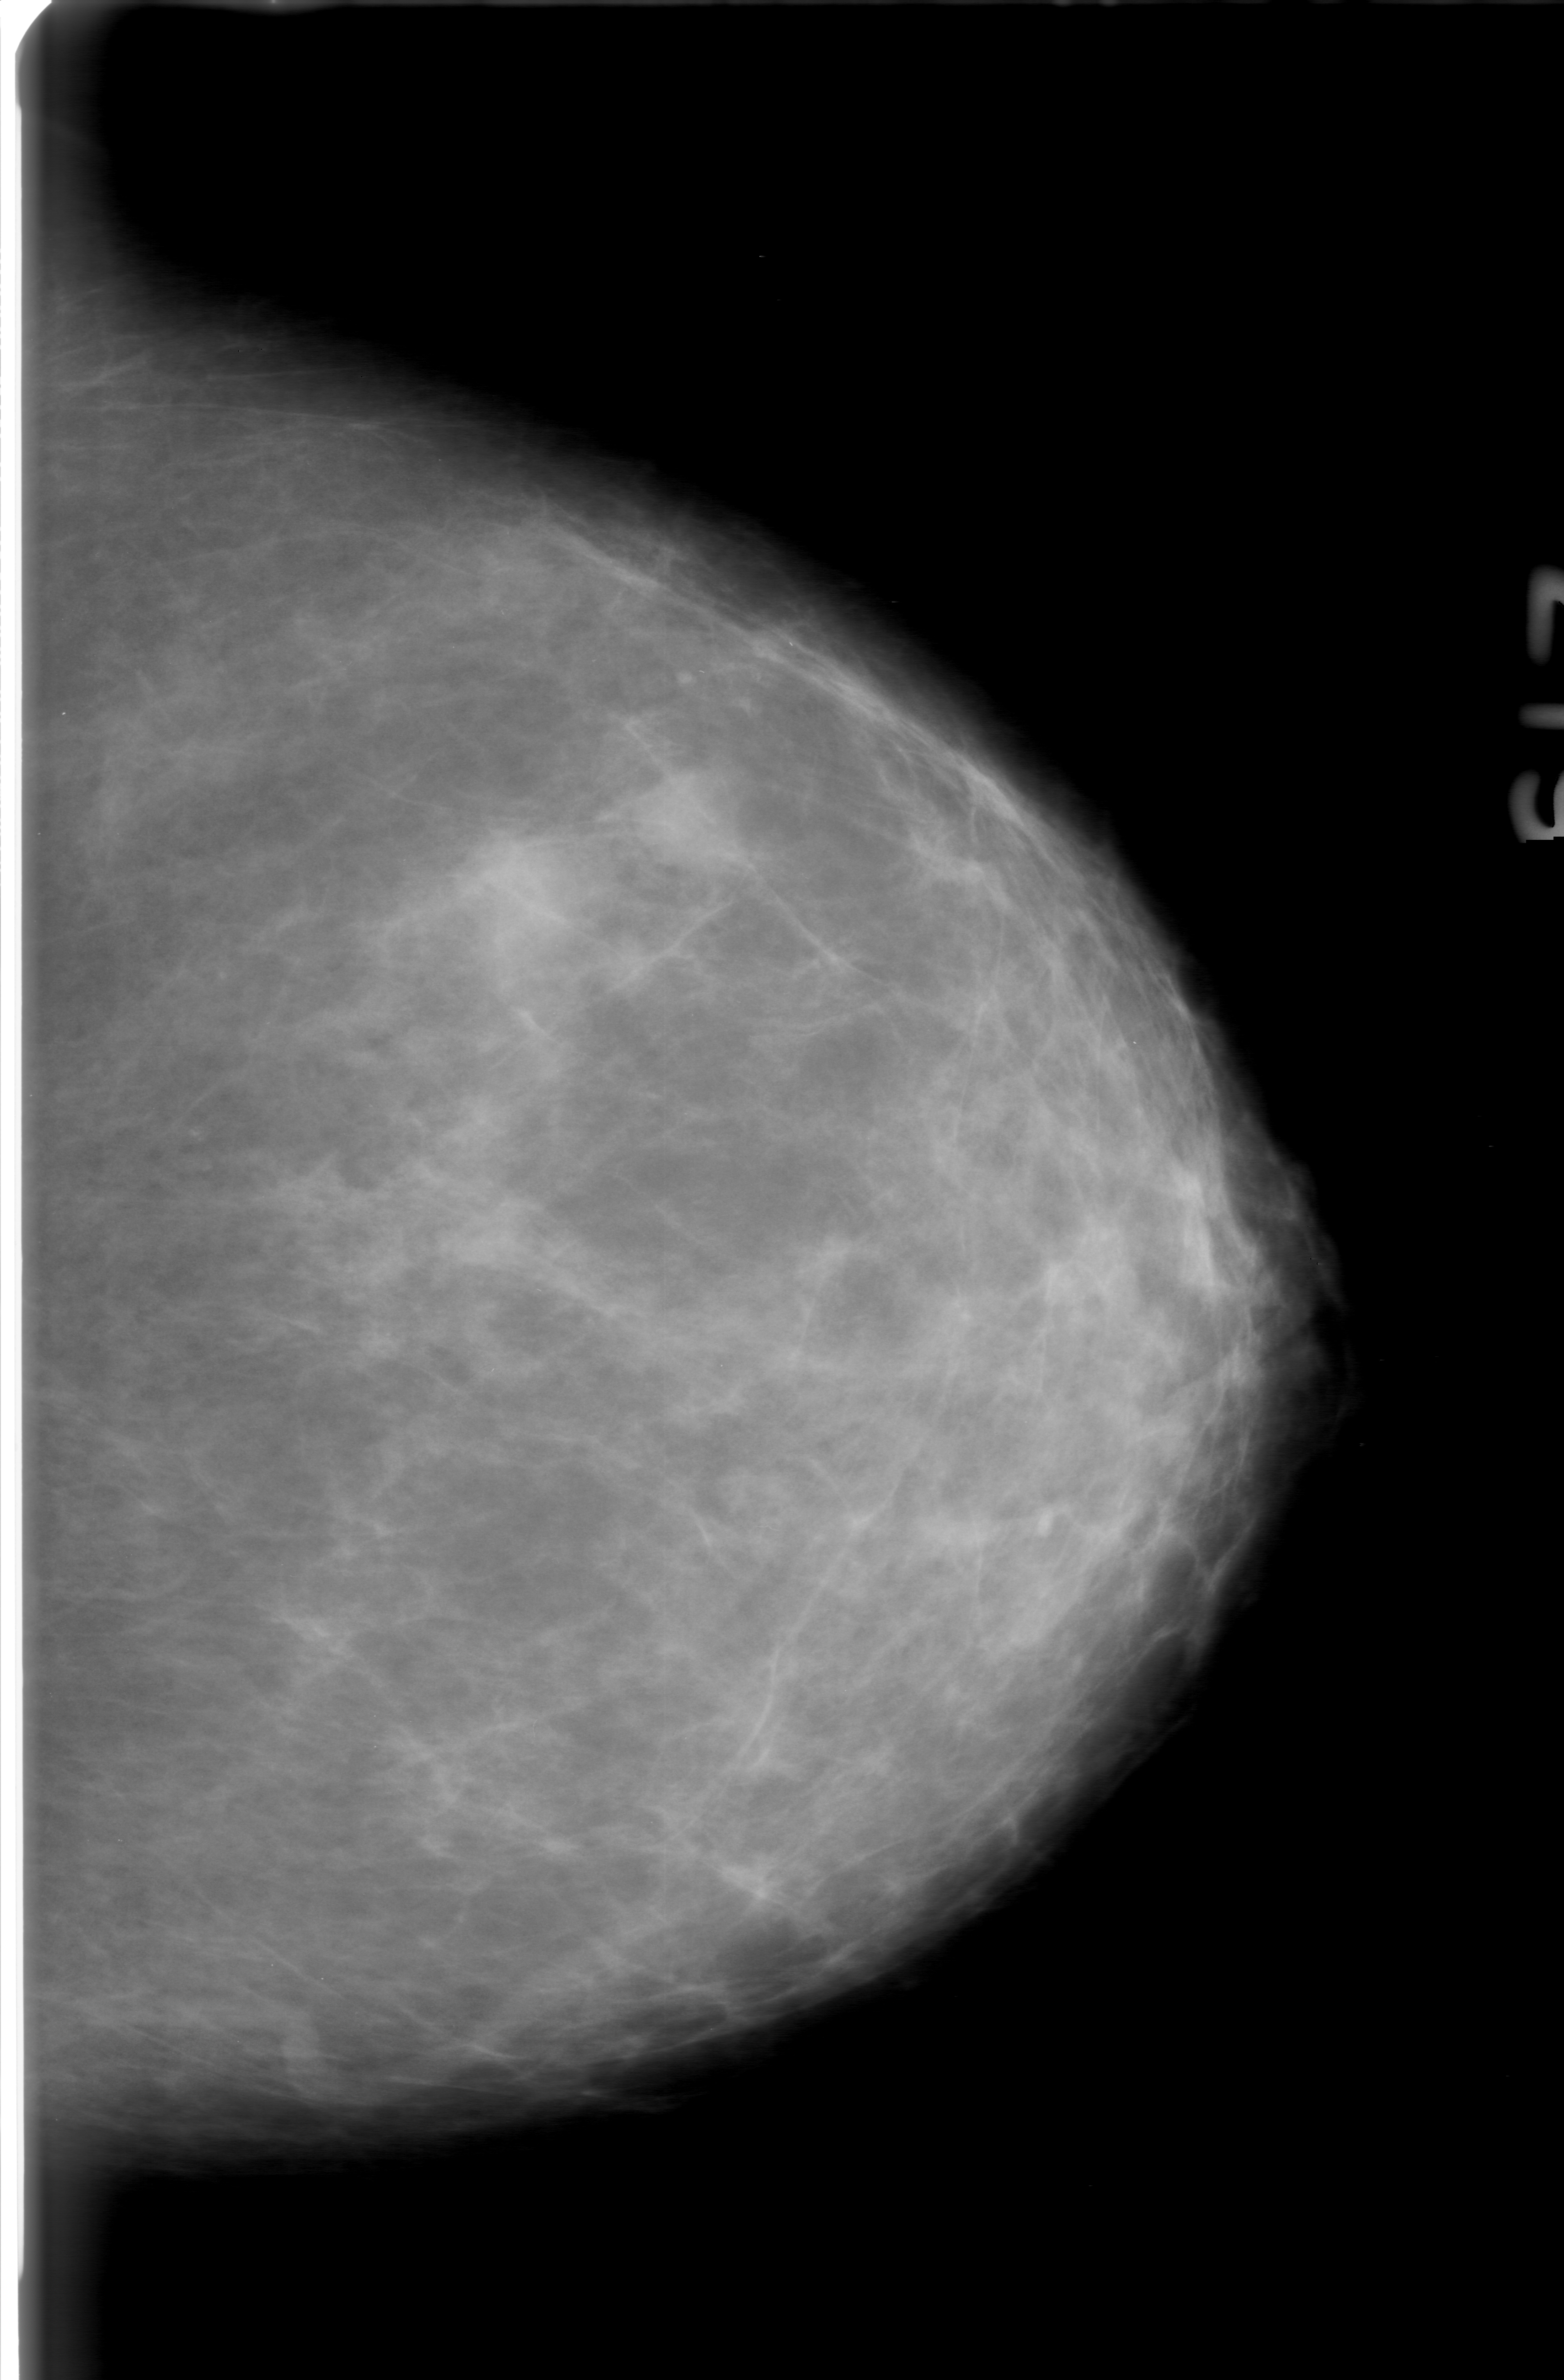
Mammogram (digitized film). Left breast. Craniocaudal (CC) view. Breast composition: scattered fibroglandular densities (BI-RADS density category 2 of 4). 1564 × 2380 image matrix.
Expert-marked regions of interest on this image (one box per marked abnormality):
- mass, shape lobulated, margins obscured; BI-RADS assessment category 0 (incomplete: needs additional imaging); subtlety rating 4 on a 1 (subtle) to 5 (obvious) scale; pathology (as recorded): benign: box from (x=593, y=749) to (x=751, y=887) px